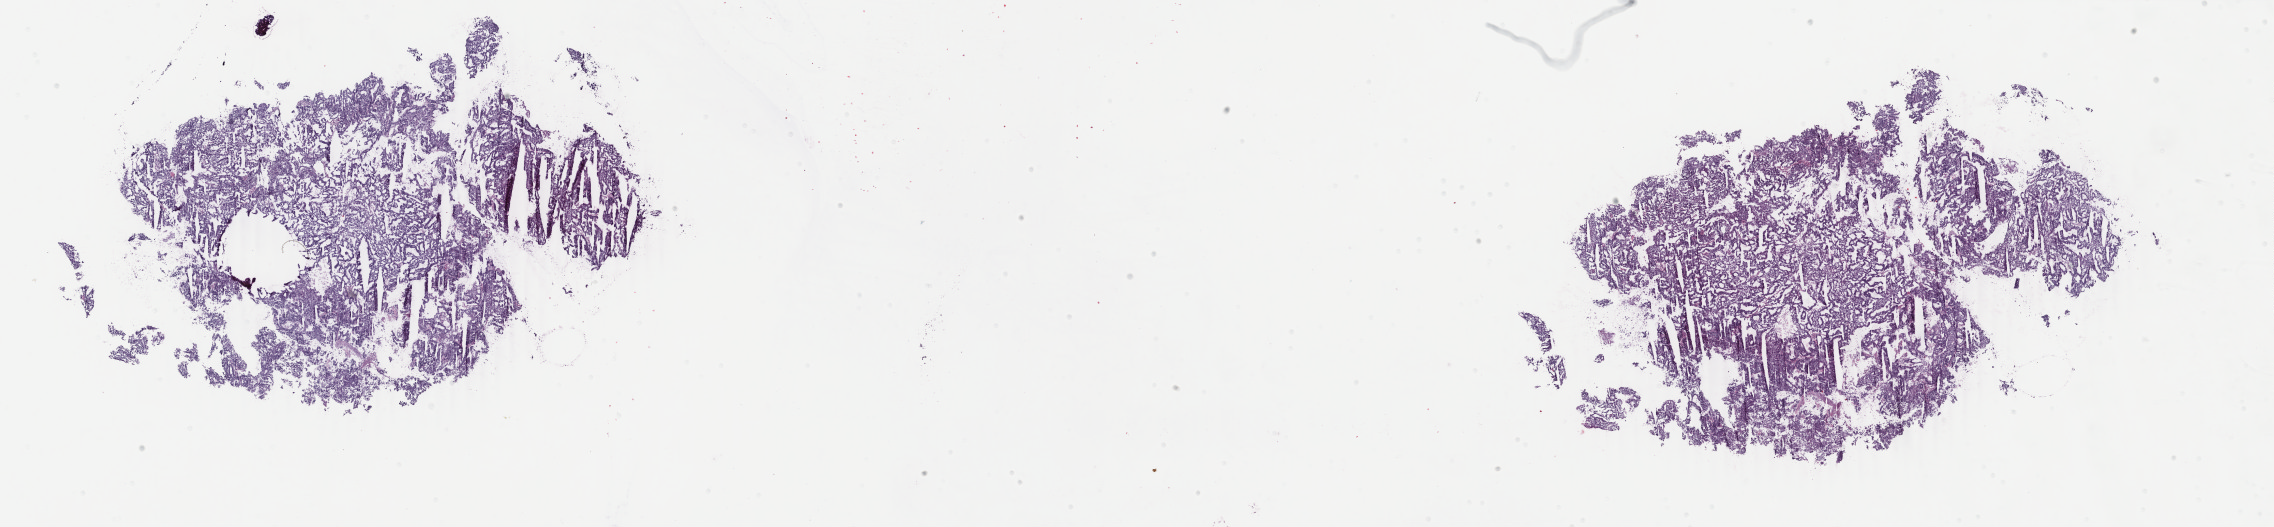
H&E-stained whole-slide image — whole scanned area (about 36.2 x 8.4 mm) shown as a low-resolution overview; frozen section from the top of the tissue portion; primary tumour sample from the uterus. Female, age 67 years at initial diagnosis. Histologic grade: G1 (well differentiated). Composition of this section per pathologist review: tumour cells 92%, tumour nuclei 95%, normal cells 0%, stromal cells 3%, necrosis 5%. Infiltration values recorded for this section: lymphocyte infiltration 1%, monocyte infiltration 1%, neutrophil infiltration 0%.
FIGO stage: IA. Pathologic diagnosis: Endometrioid adenocarcinoma, NOS (endometrium).